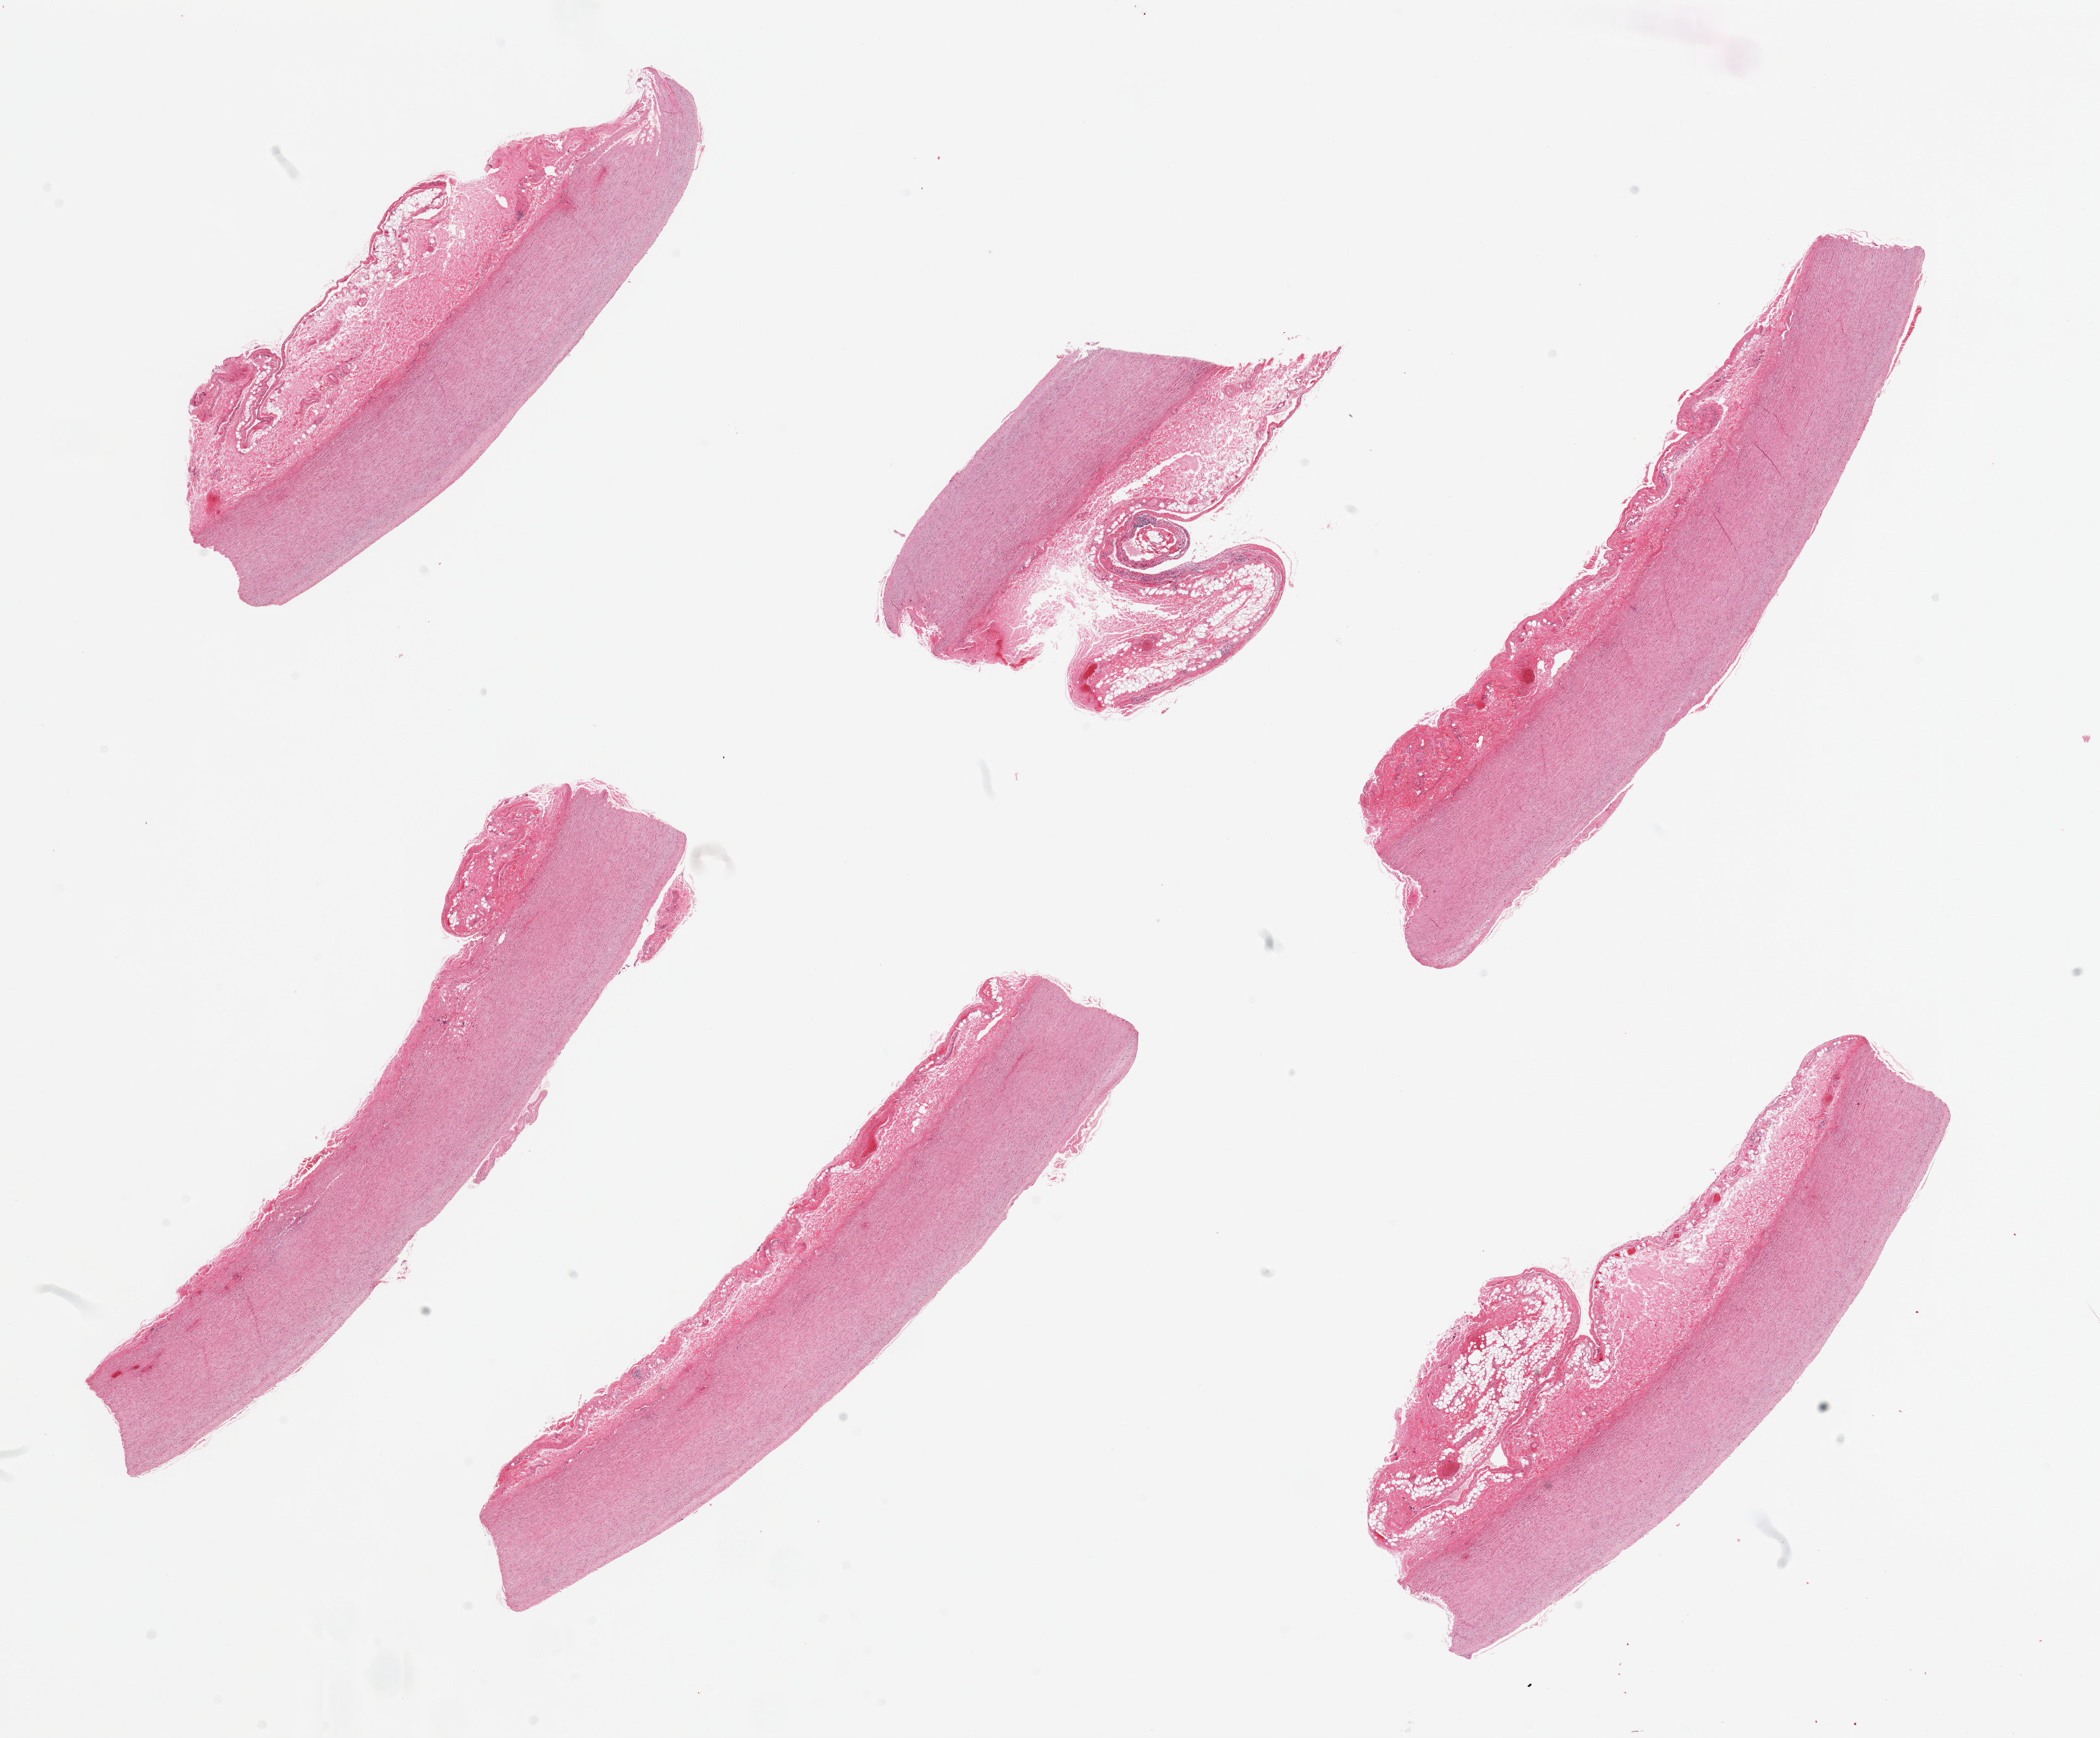
H&E whole-slide image, brightfield, low-resolution overview of the scanned area, about 25.6 x 21.2 mm. PAXgene-fixed, paraffin-embedded tissue. Section of aorta (target tissue). Donor tissue sample.
Reviewer comment on this tissue sample: 6 pieces, up t0 ~1.5mm adherent serosa/fat.